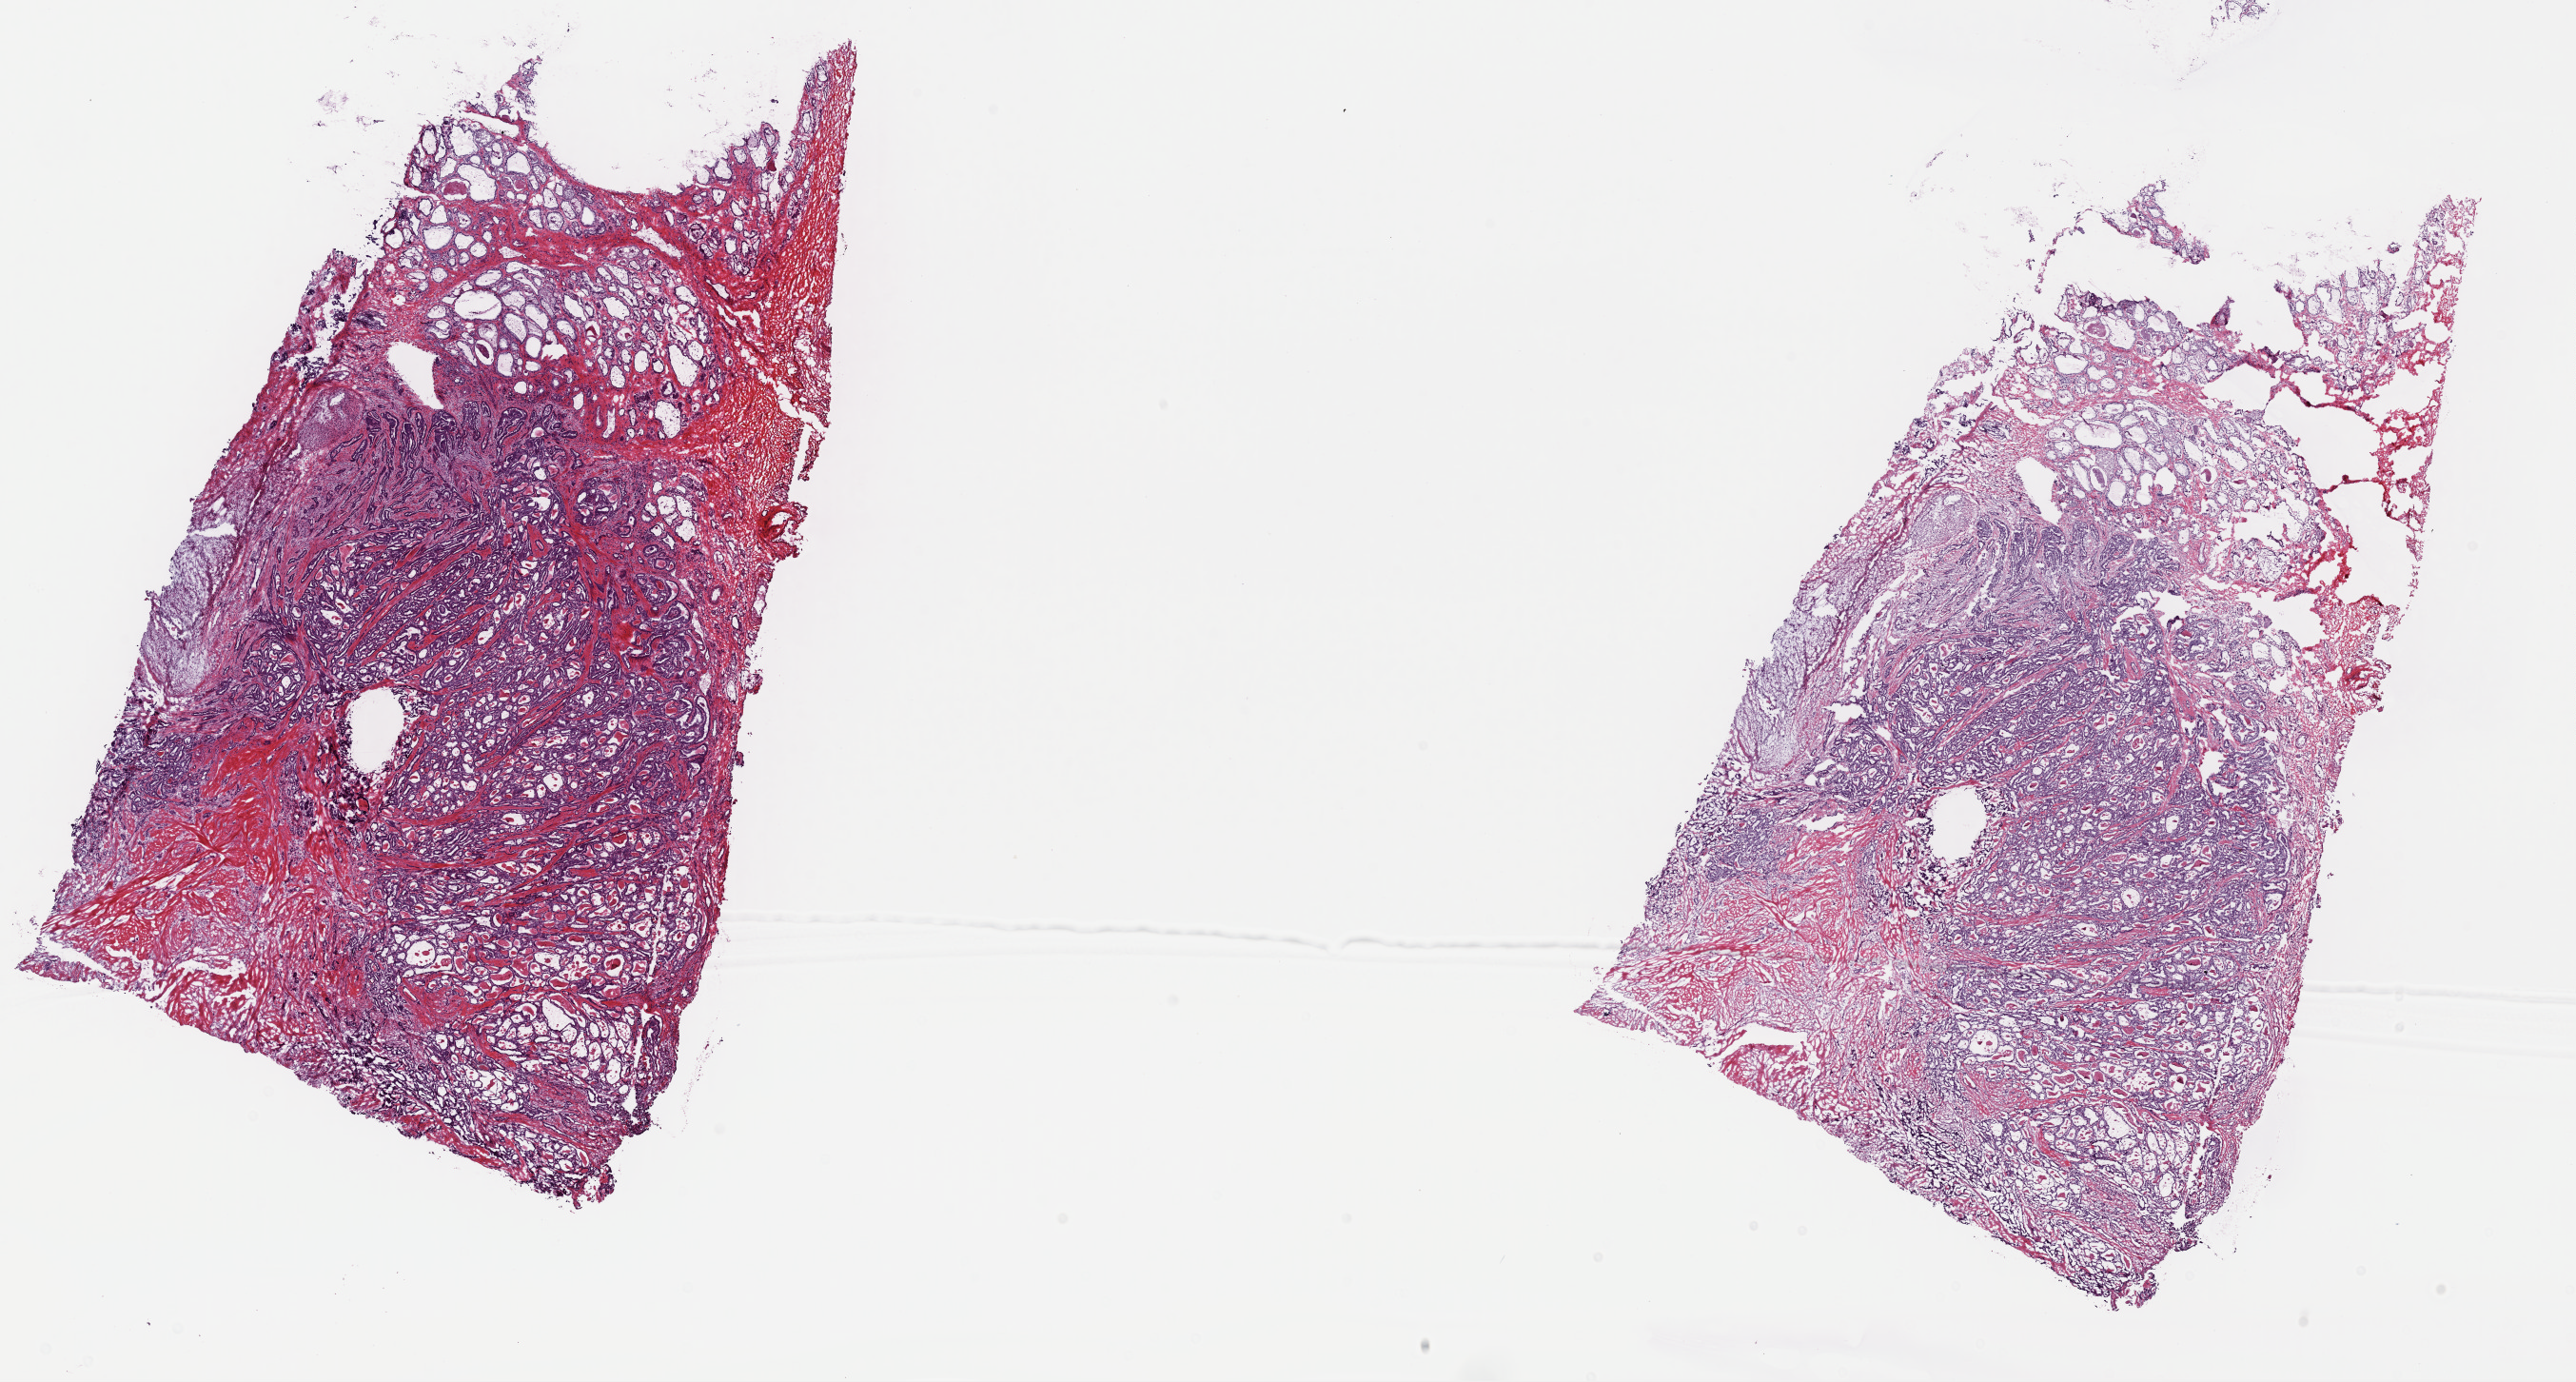
Whole-slide histology image, H&E-stained, low-resolution overview of the scanned area, about 21.4 x 11.5 mm (slide scanned at 40x), frozen section from the top of the tissue portion, thyroid, primary tumour sample. Male patient; age at initial diagnosis 33 years. Slide review estimates, as recorded: tumour cells 80%, tumour nuclei 70%, normal cells 15%, stromal cells 5%, necrosis 0%. Infiltration values recorded for this section: lymphocyte infiltration 0%, monocyte infiltration 0%, neutrophil infiltration 0%.
Laterality: right. TNM: T2 N1 MX. Pathologic diagnosis: Papillary adenocarcinoma, NOS. Lymph nodes positive (case pathology): 1 of 2 examined. AJCC pathologic stage: I (7th edition).